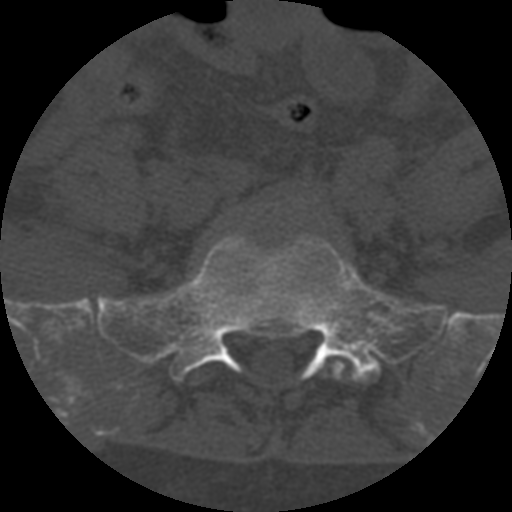
CT including the spine, one axial slice; position 171 of 708 along the scan axis; reconstruction kernel STANDARD; 120 kVp; one of 3 acquisitions stored at this slice position; bone window (W 1800 / L 400 HU); 512 × 512 image matrix, field of view 160 × 160 mm. Patient age 55 years. Case-level facts recorded for this patient, not image findings: primary cancer: colon; vertebrae with lytic lesions (as recorded): T12, L1, L5.
Outlined on this slice (semi-automatically segmented with operator editing):
- L5 vertebra: bounding box [x1, y1, x2, y2] px = [323, 362, 345, 380]